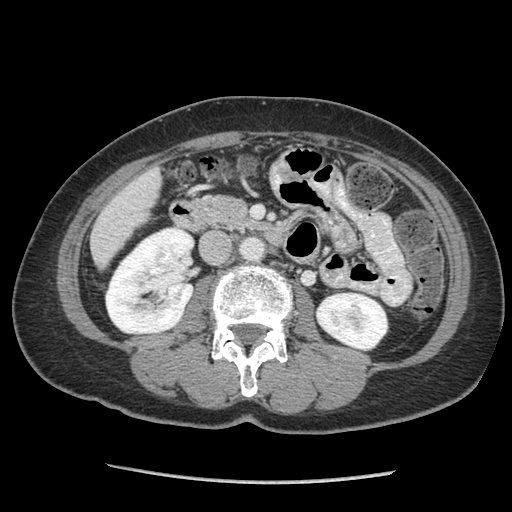
Contrast-enhanced abdominal CT (liver protocol), one axial slice; position 21 of 105 along the scan axis; reconstruction kernel STANDARD; 140 kVp; soft-tissue window (W 400 / L 40 HU); 2.5 mm slice thickness; 512 × 512 image matrix. From the clinical record (not read from this slice): diagnosis: hepatocellular carcinoma (patient treated with transarterial chemoembolisation; whether this scan precedes or follows treatment is not stated here); TNM stage (as recorded): Stage-I; Child-Pugh class: A; tumour nodularity: uninodular; tumour size: 11.1 cm.
Annotated regions visible in this slice (semi-automatic segmentation, software-assisted and operator-edited):
- liver parenchyma outside the tumour (the mass and vessels are separate outlines, so this box may not span the whole liver): box from (x=90, y=168) to (x=160, y=266) px